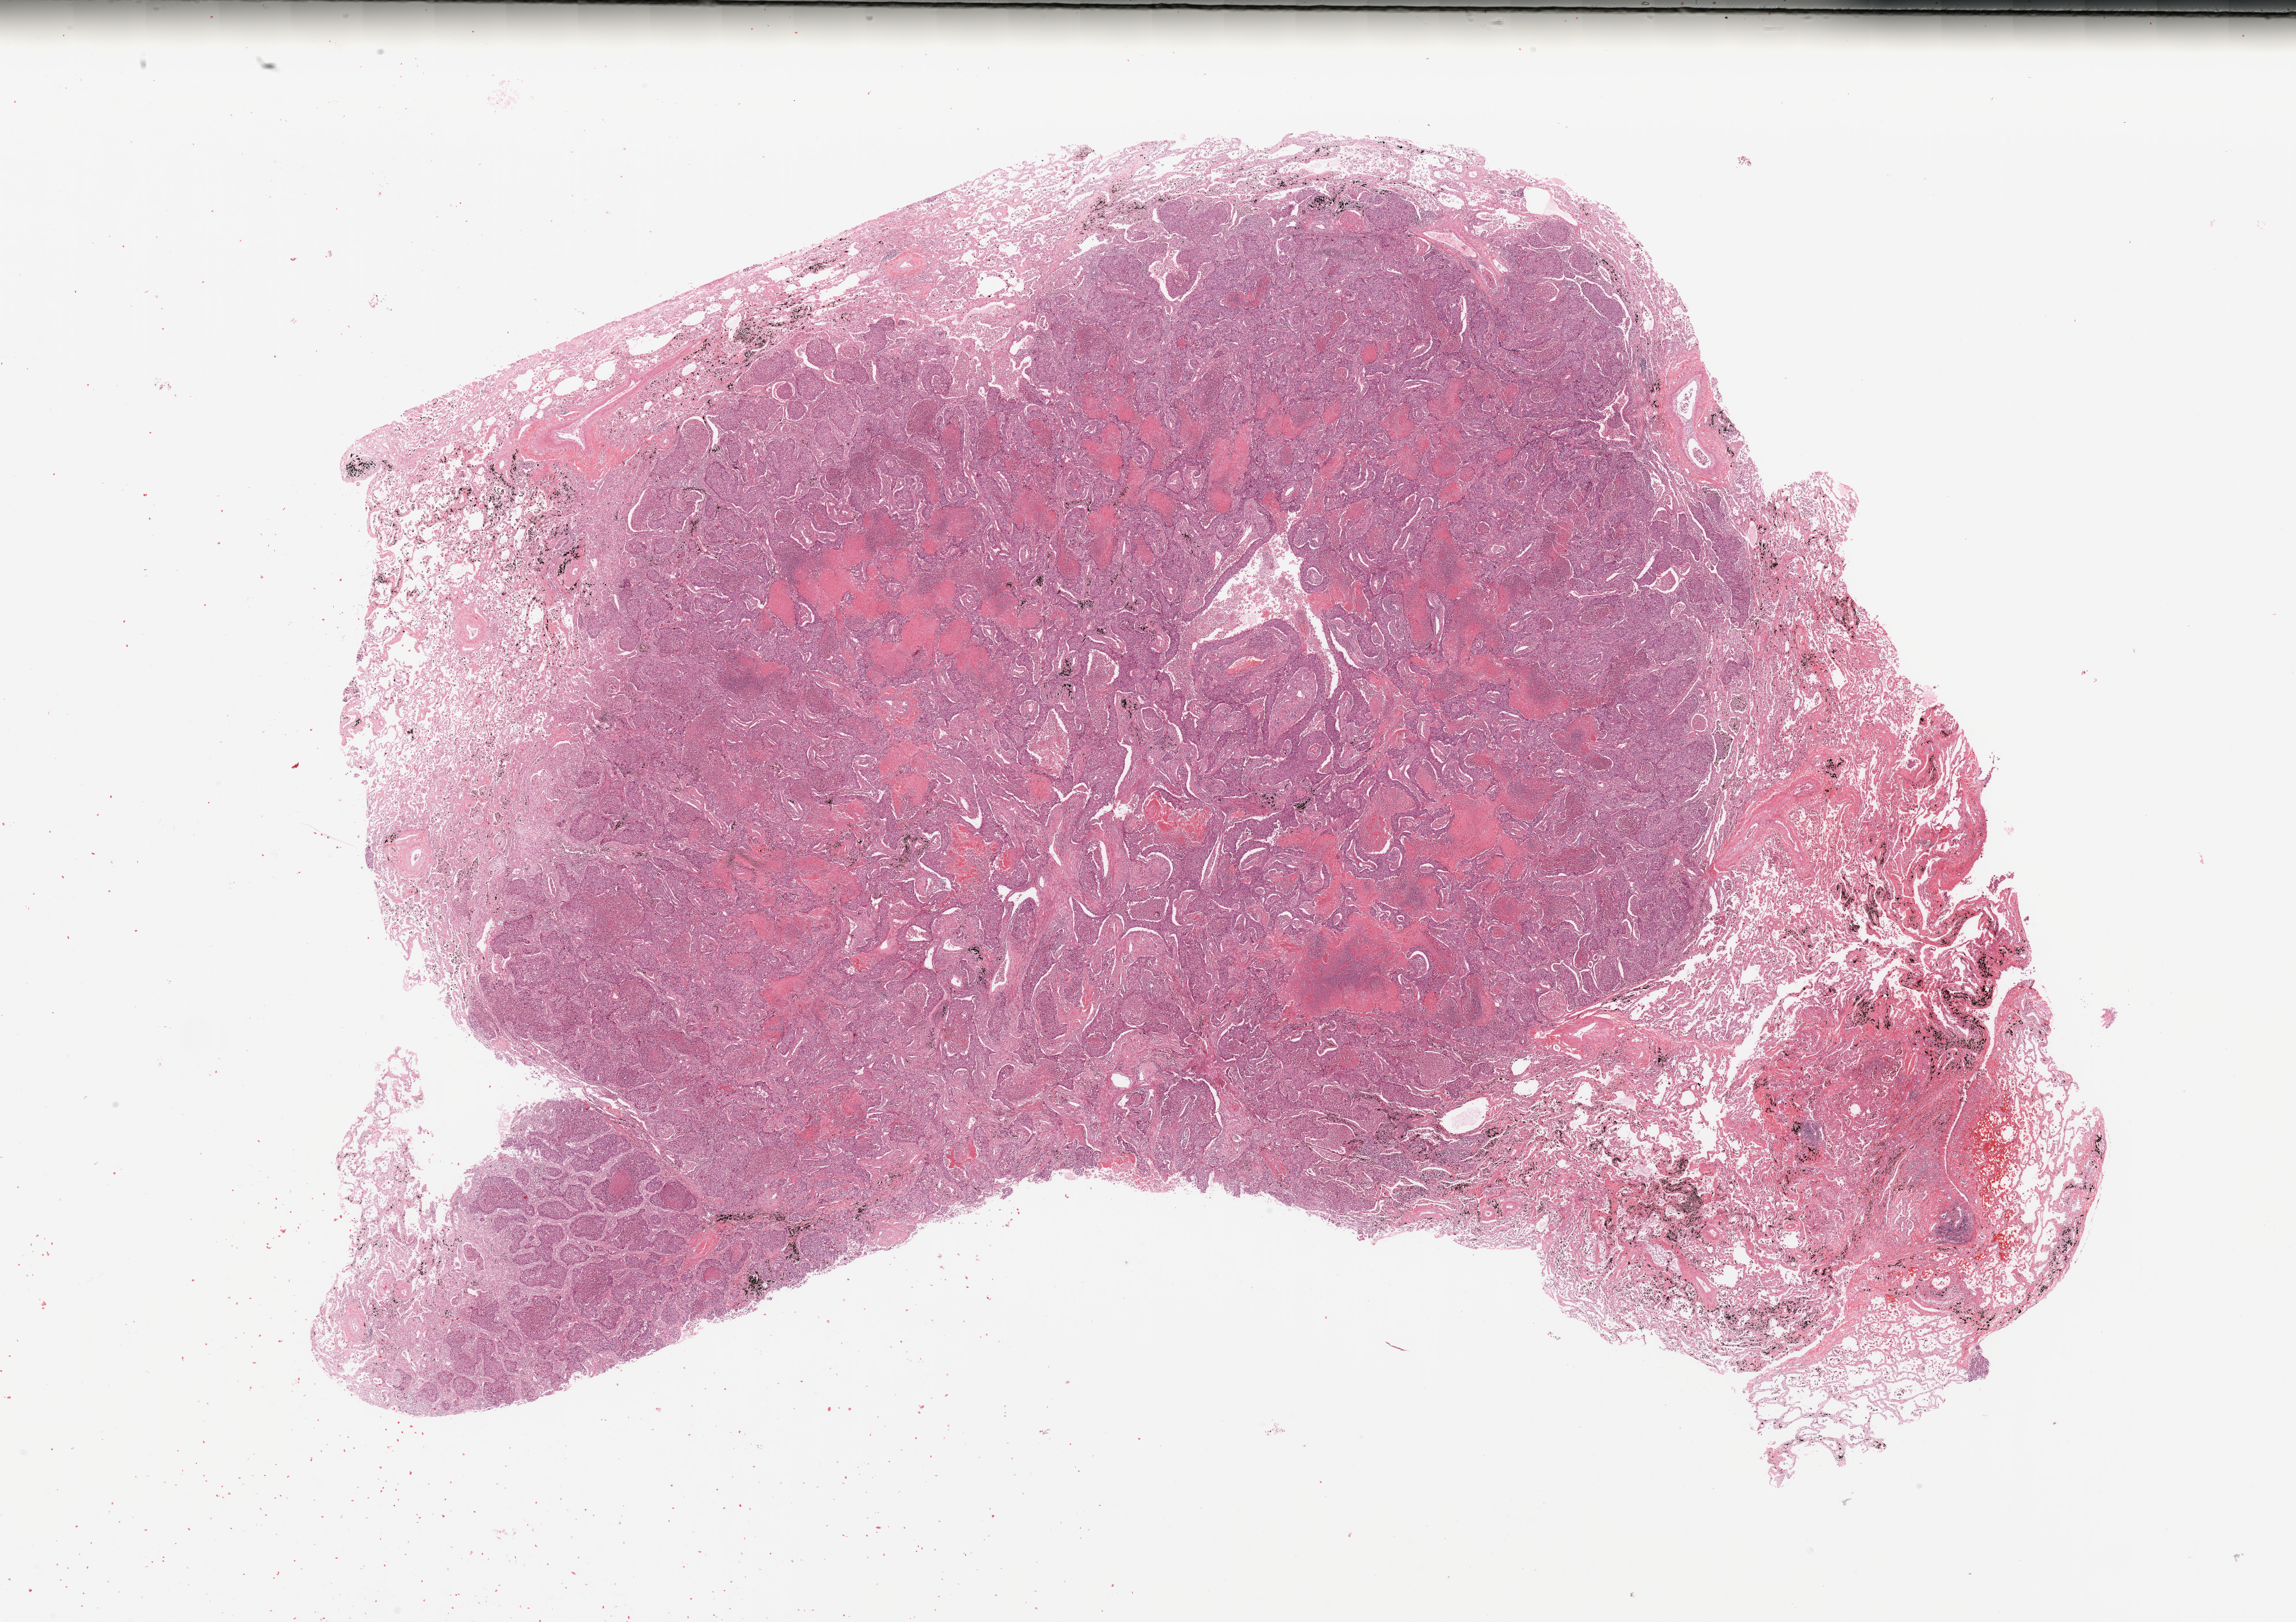
H&E whole-slide image, shown as a low-resolution overview of the whole scanned area (about 31.5 x 22.2 mm), lung, tumour tissue. 65-year-old male patient. Histologic grade: G3 (poorly differentiated).
* diagnosis: Squamous cell carcinoma, NOS
* AJCC pathologic stage: IB